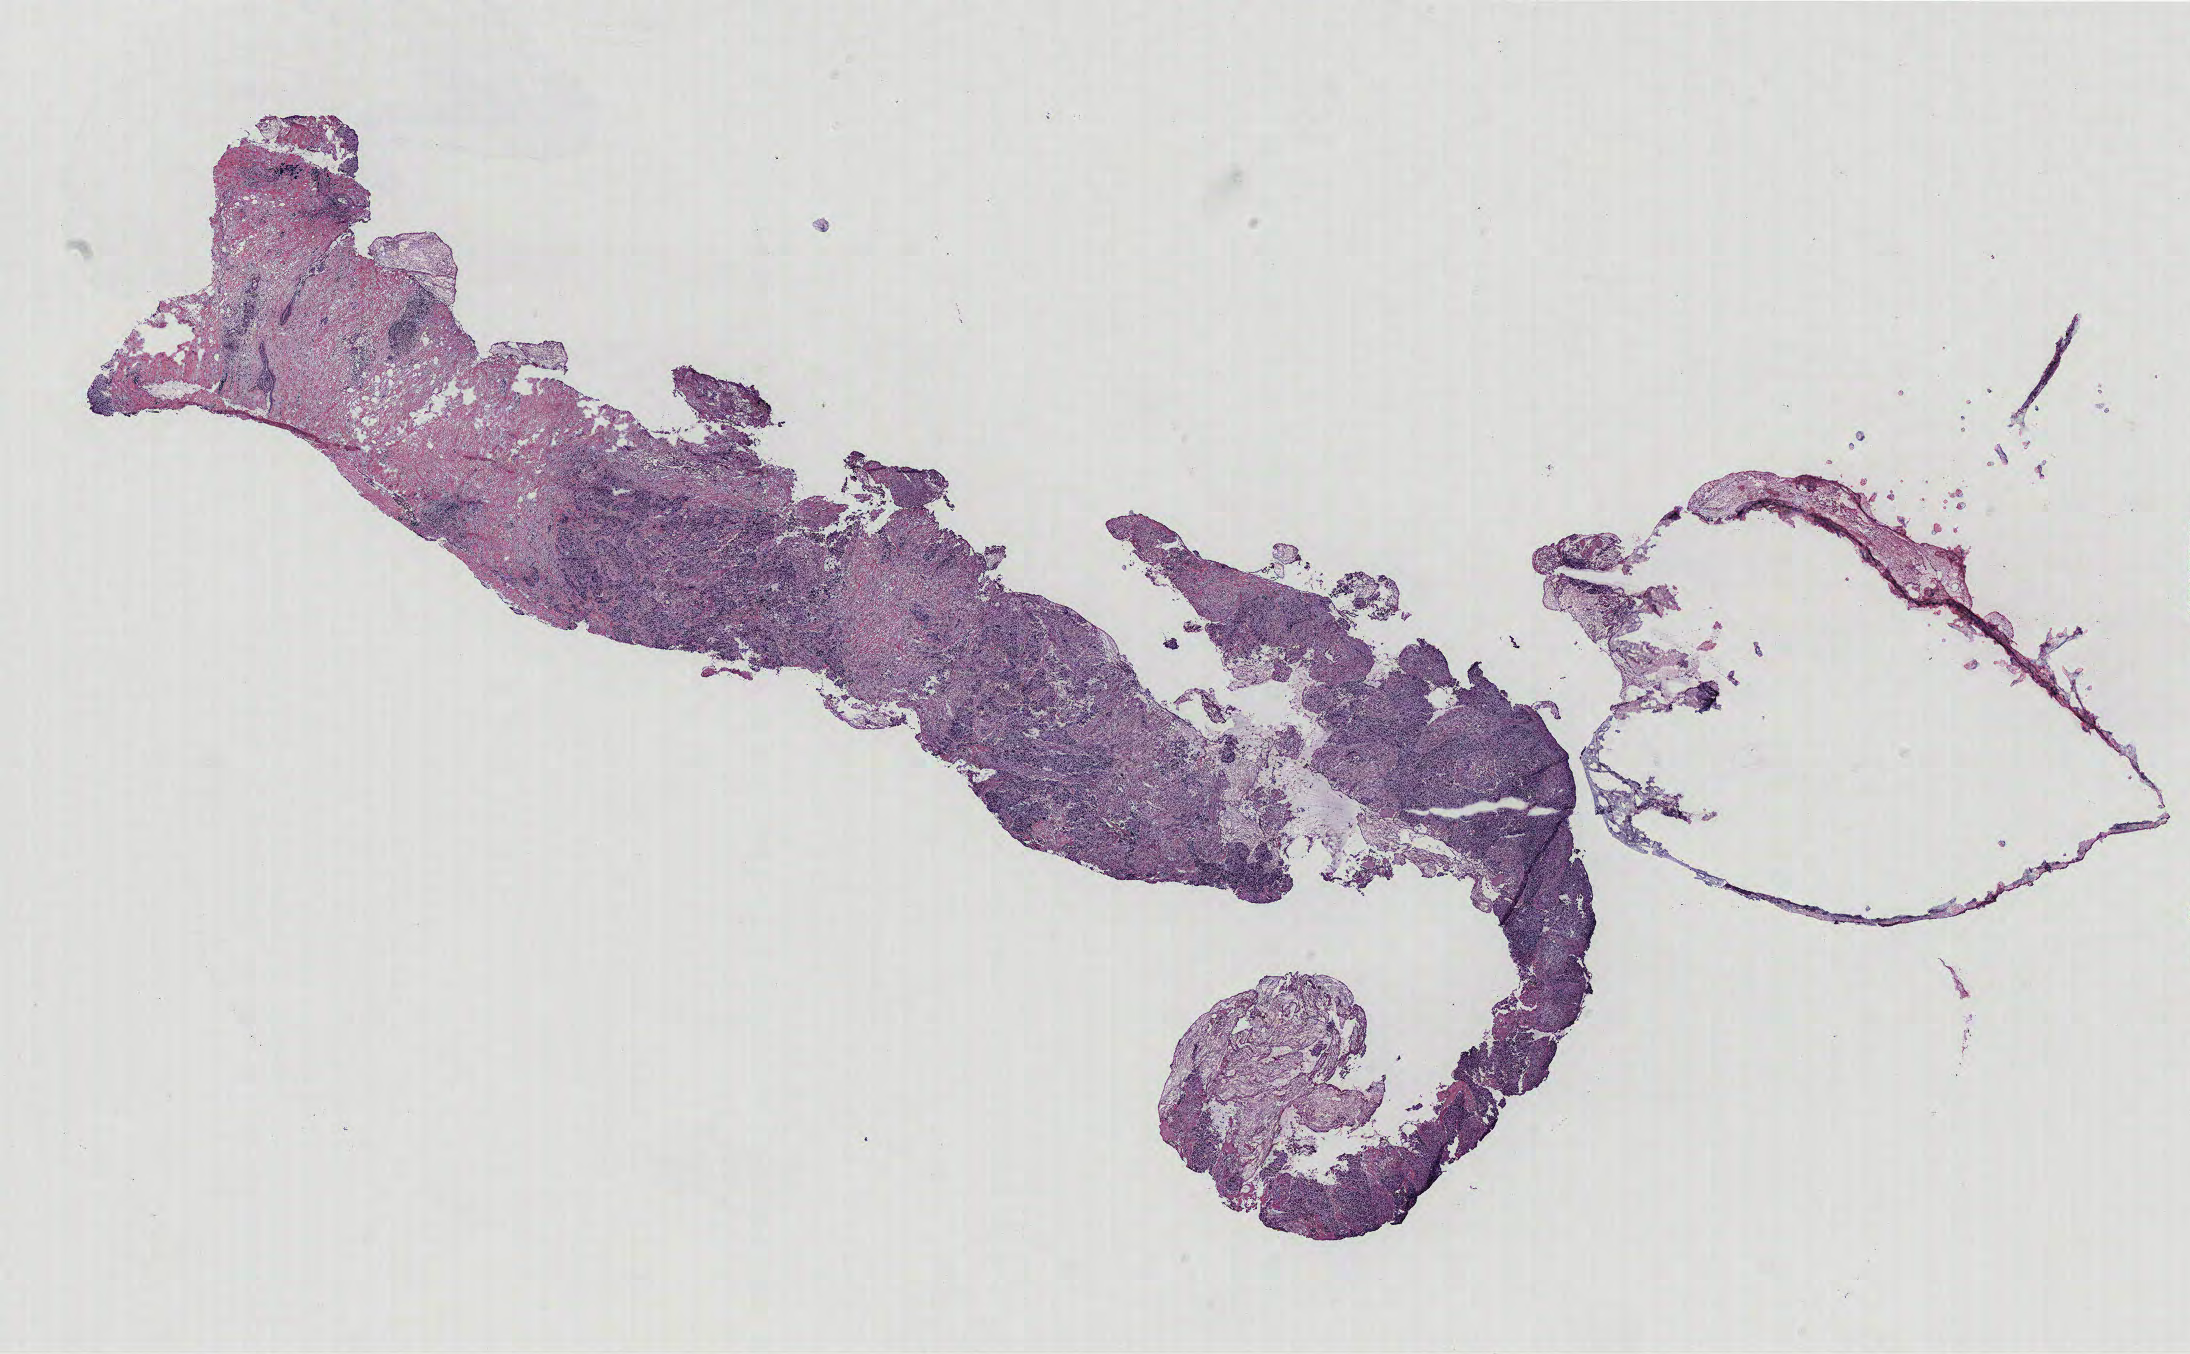
Whole-slide histology image, Hematoxylin and eosin (H&E) stained — a low-resolution overview of the entire scanned area, about 17.5 x 10.8 mm. Tumour tissue sample, breast. Patient: female, age 61 years.
- AJCC pathologic stage: III
- histologic diagnosis: Infiltrating duct carcinoma, NOS